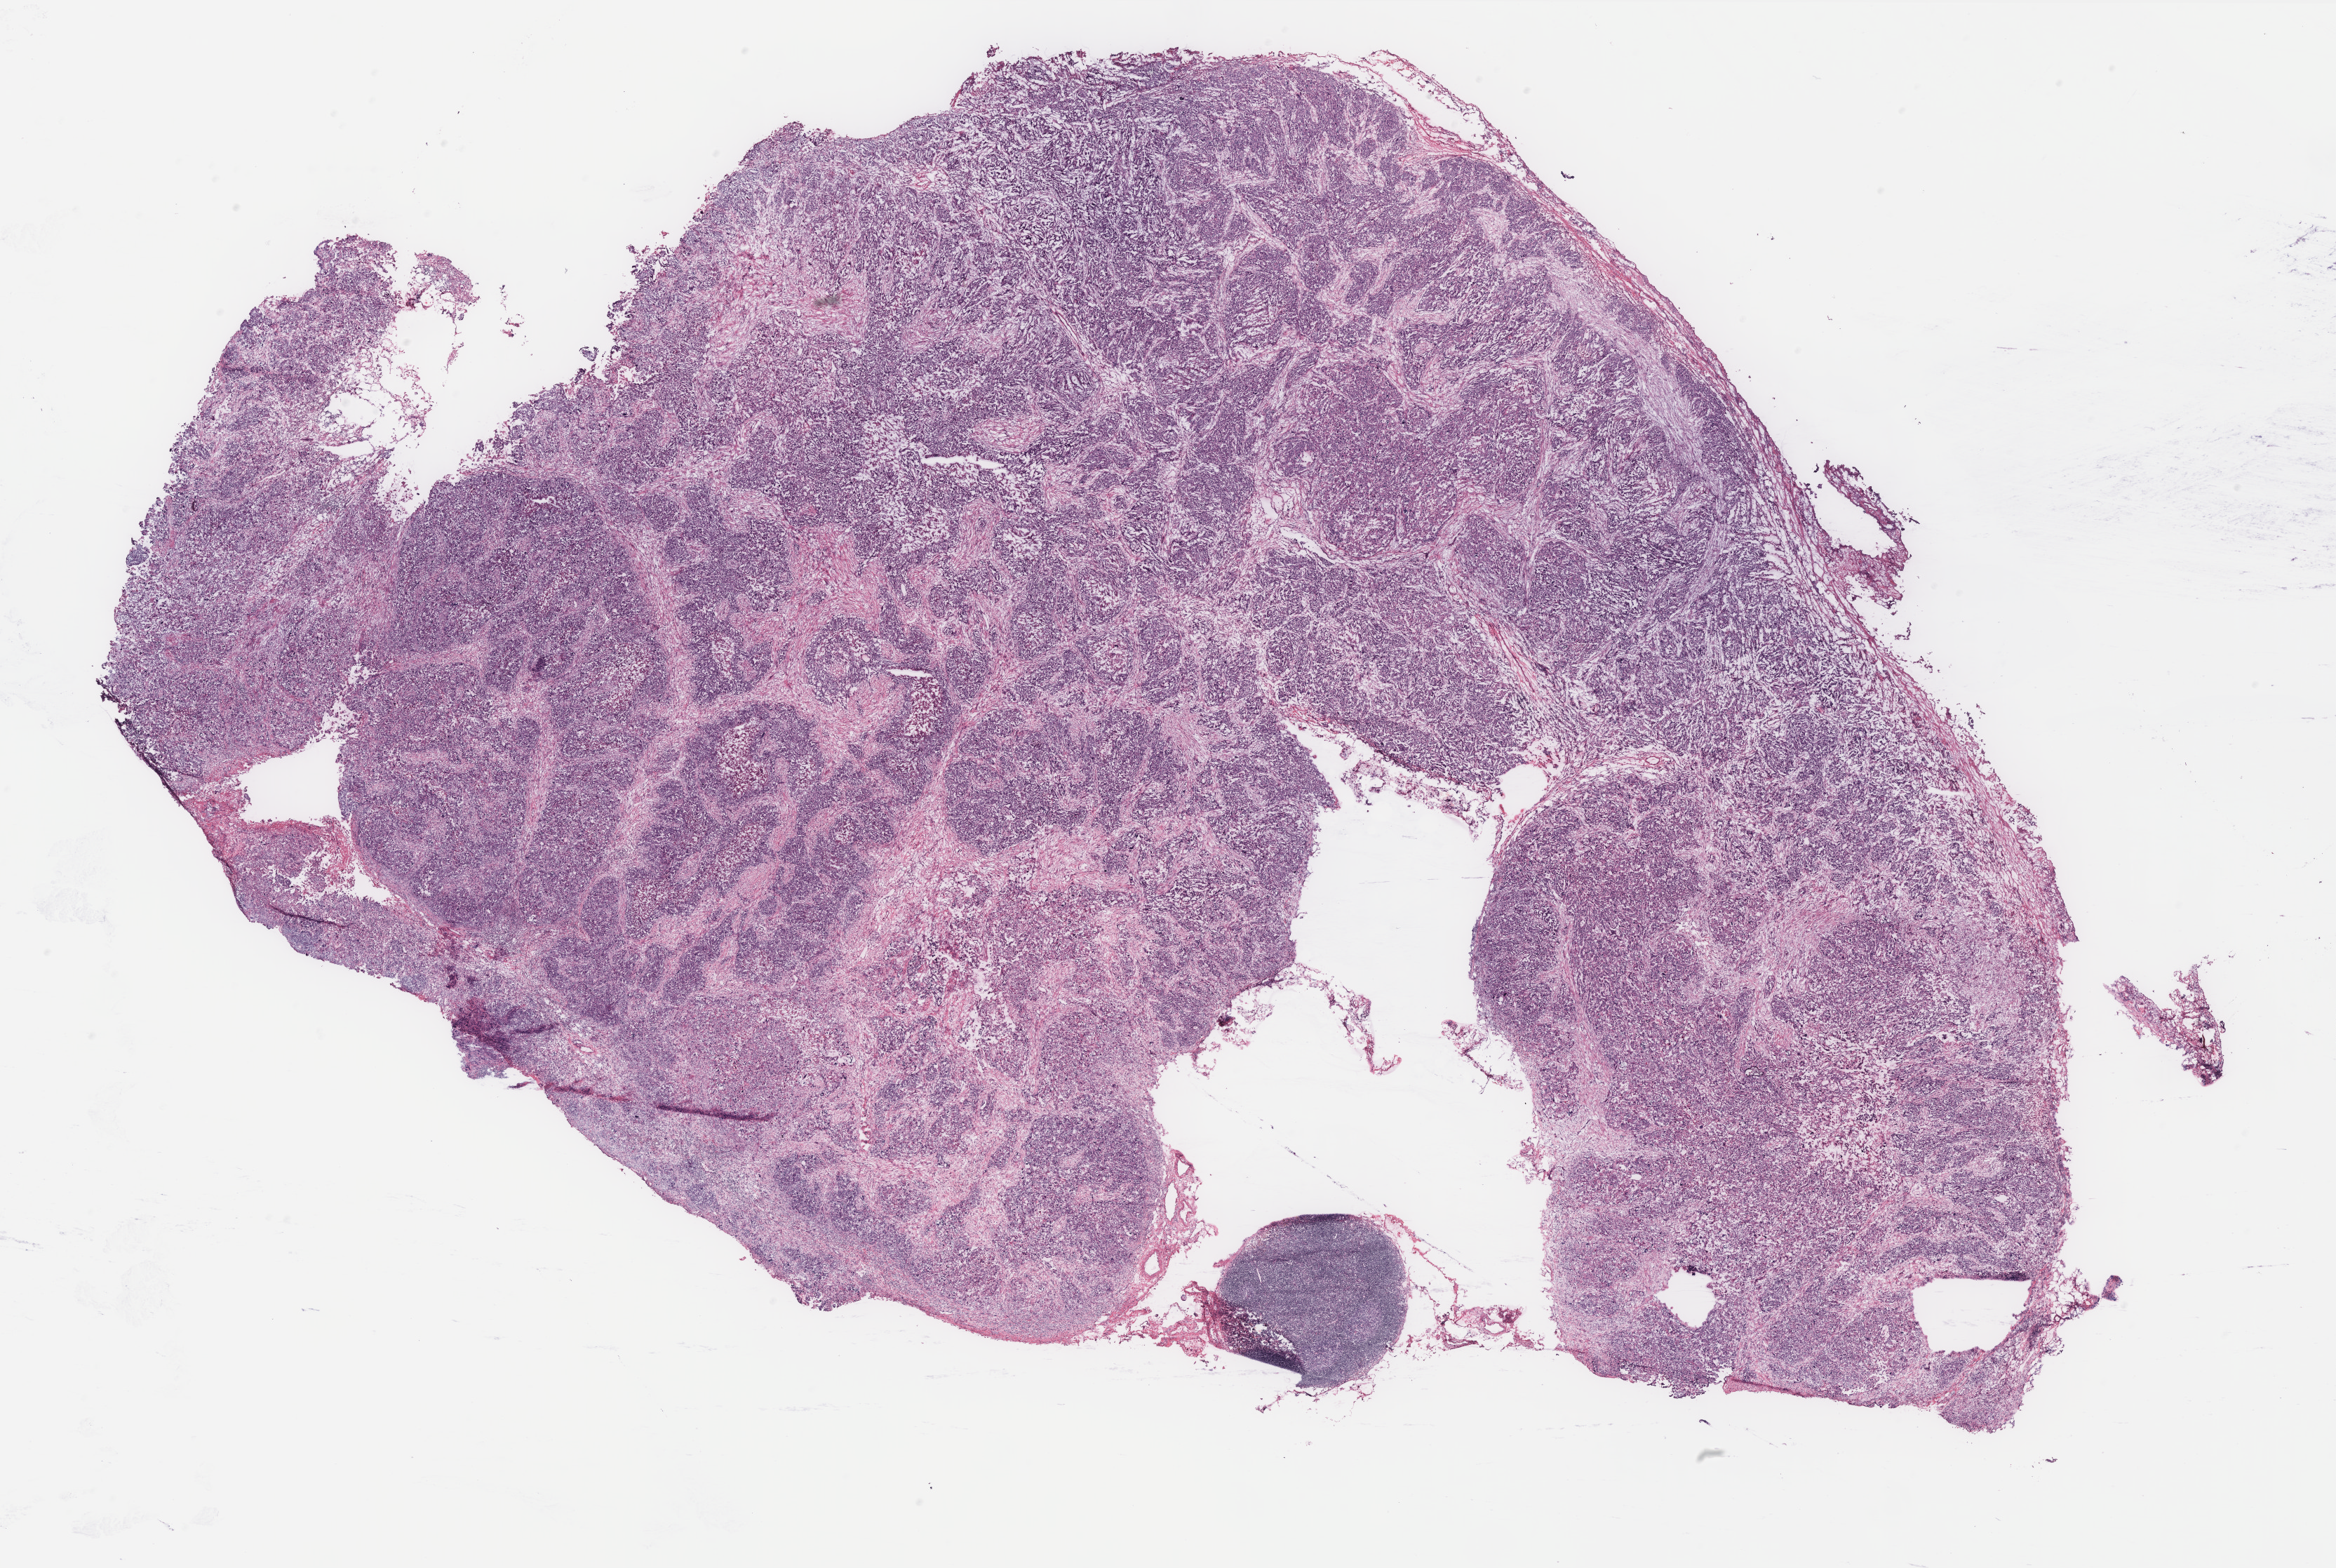
H&E whole-slide image — shown as a low-resolution overview of the whole scanned area (about 26.7 x 17.9 mm); ovary, tissue type not recorded. Patient sex: female.
Patient diagnosis: Serous adenocarcinoma, NOS.